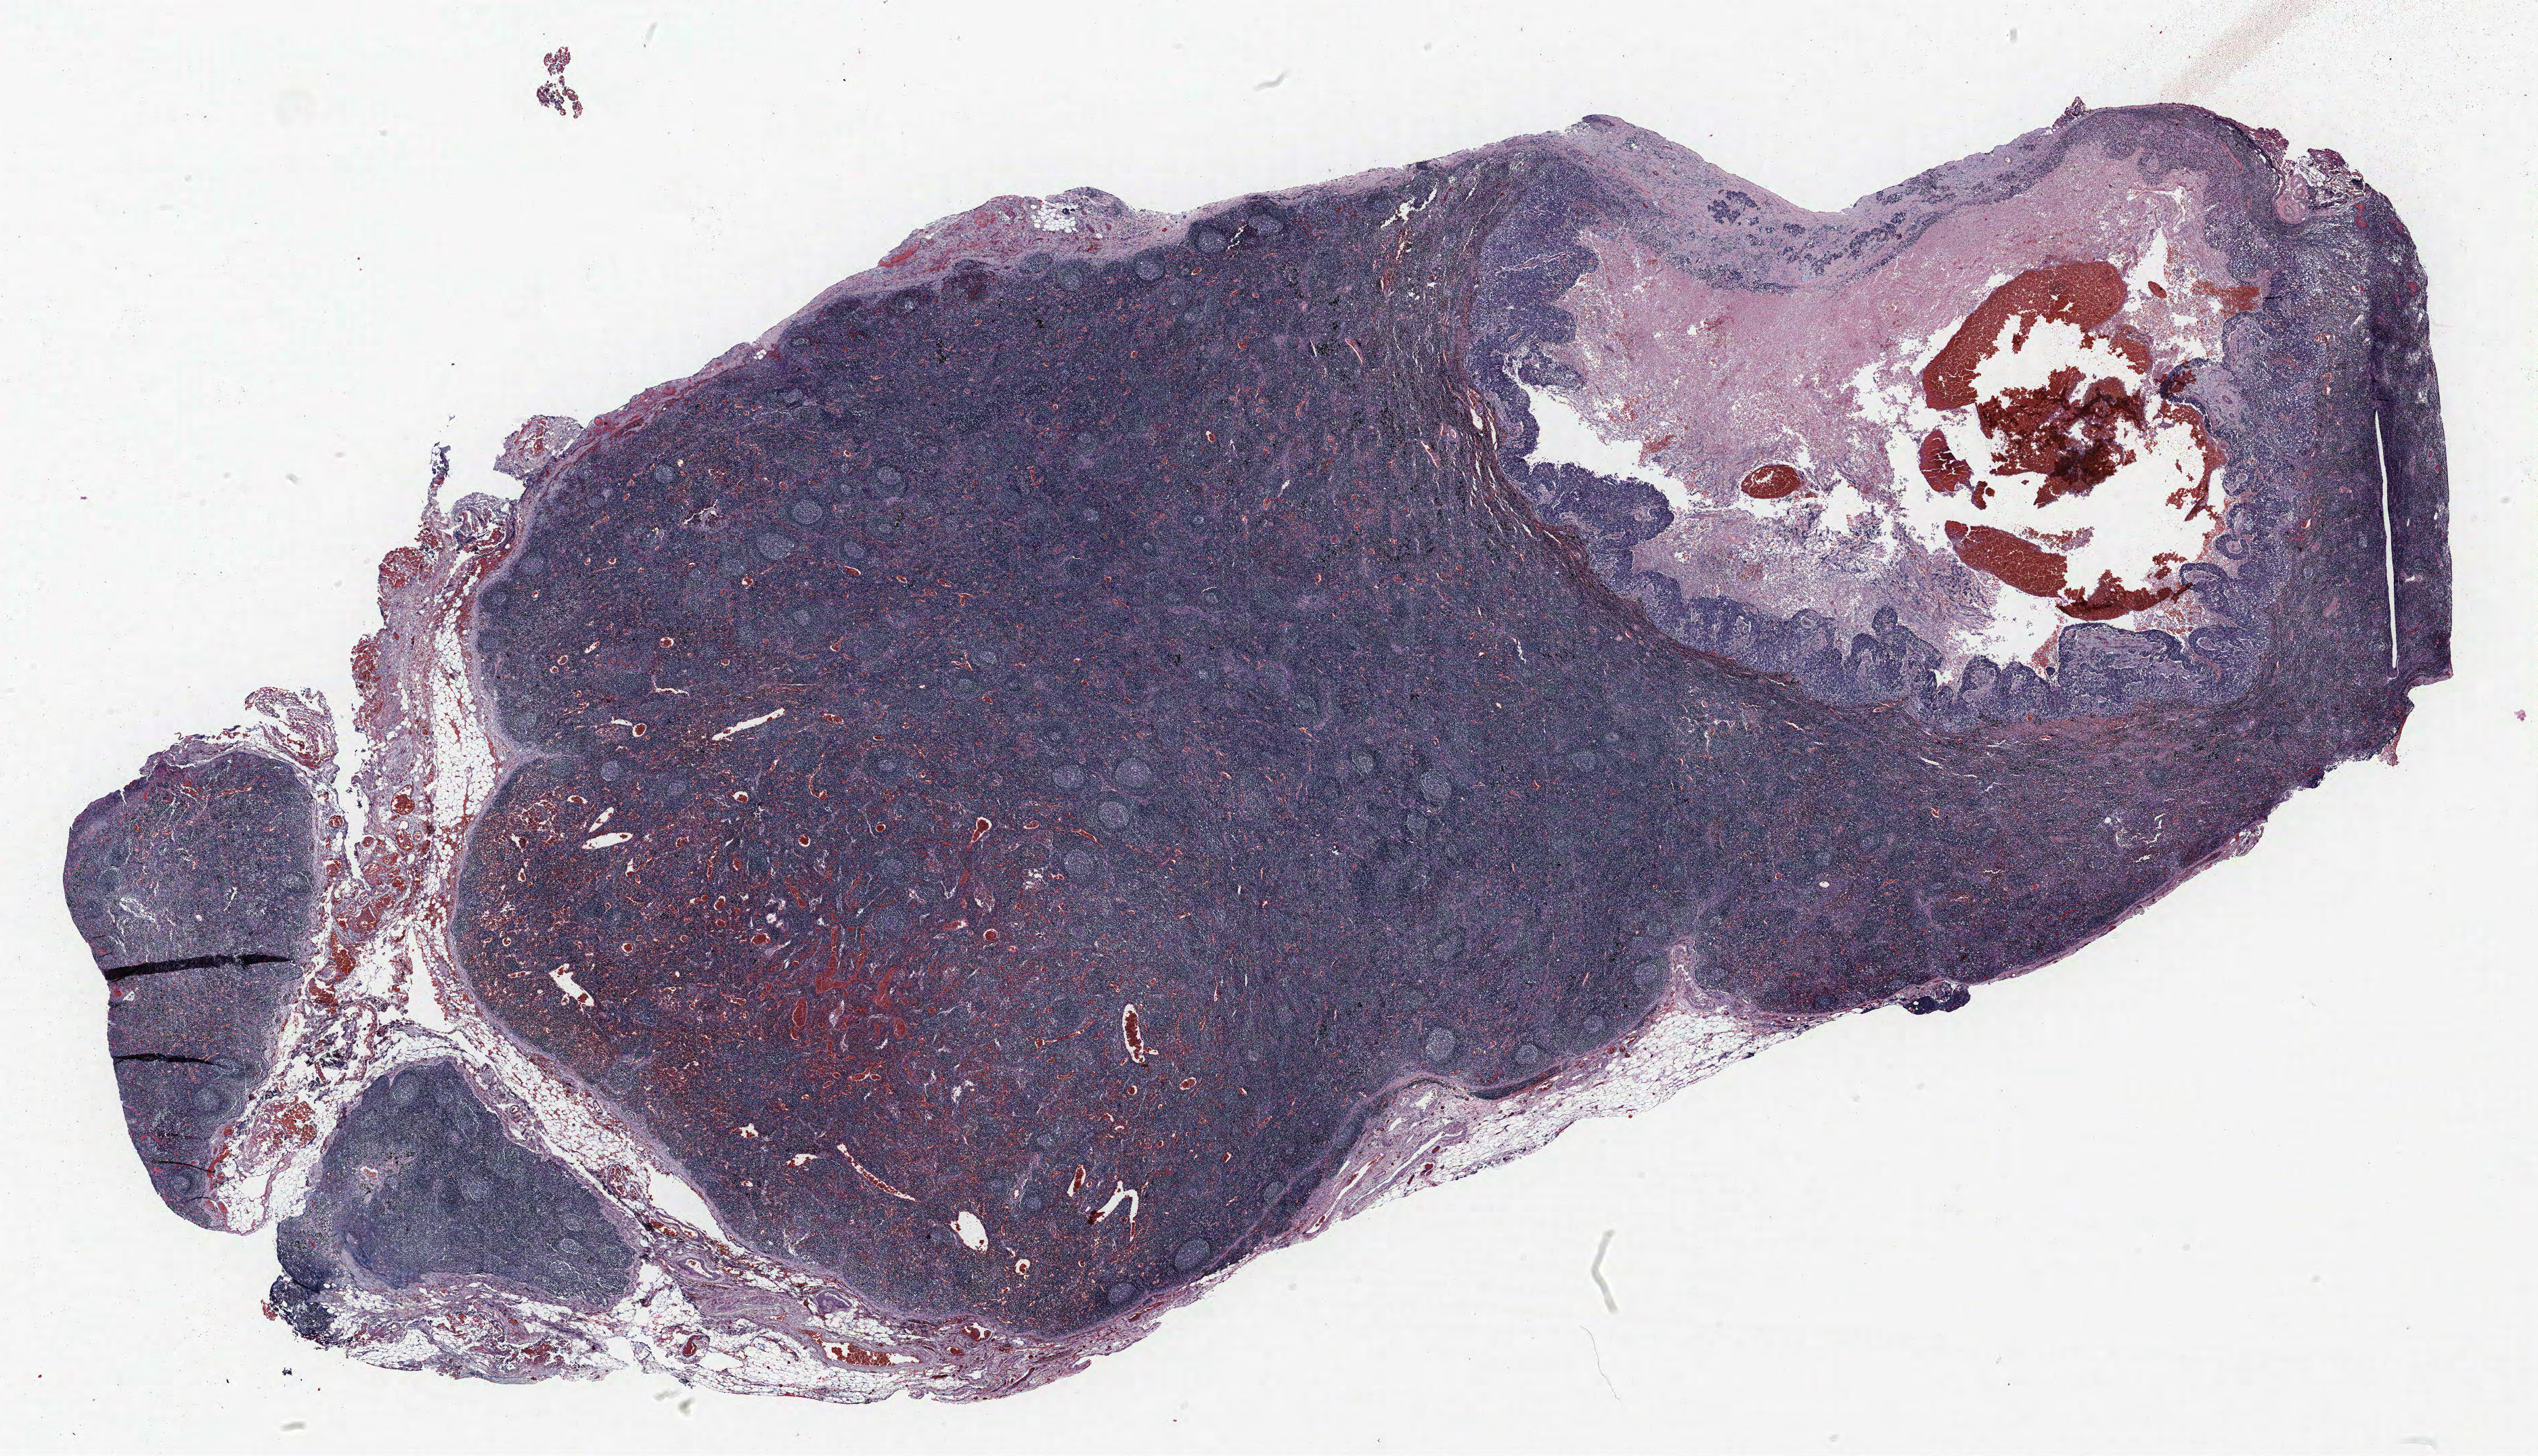
Whole-slide histology image, Hematoxylin and eosin (H&E) stained — a low-resolution overview of the entire scanned area, about 30.0 x 17.2 mm; FFPE section; lung tissue. Female patient, aged 65 at enrolment. Former smoker at enrolment. Grade: moderately differentiated (G2).
- tumour size (pathology): 90 mm
- primary tumour location (clinical record): left lower lobe
- stage (AJCC 6th edition): IIB
- participant's lung-cancer diagnosis: Squamous cell carcinoma, NOS (ICD-O-3 8070/3)